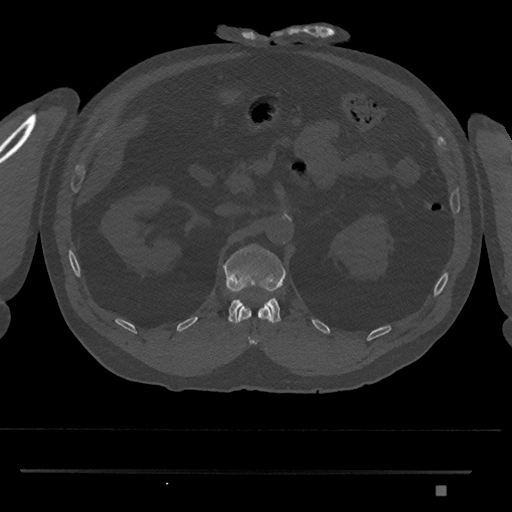
CT including the spine, one axial slice. Position 851 of 1134 along the scan axis. Reconstruction kernel Br40s/3. Bone window (W 1800 / L 400 HU). 0.5 mm slice thickness. 512 × 512 image matrix. Patient: male, 65 years. From the clinical record (not read from this slice): primary cancer: prostate.
Structures marked on this image (semi-automatically segmented with operator editing):
- L1 vertebra: bounding box (x1, y1, x2, y2) in pixels: (223, 244, 286, 324)
- T12 vertebra: (237, 305, 273, 345)